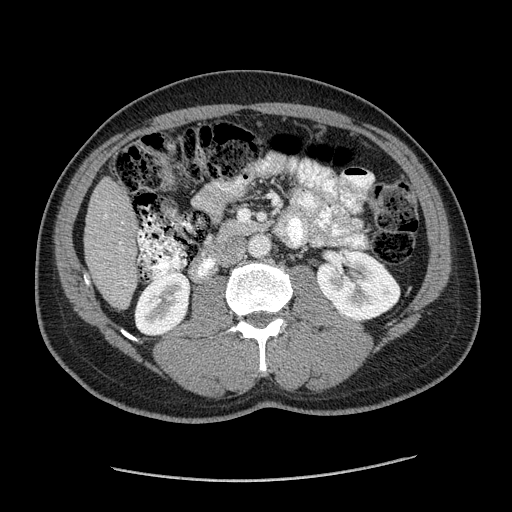
Contrast-enhanced abdominal CT (liver protocol), one axial slice; position 49 of 182 along the scan axis; reconstruction kernel STANDARD; soft-tissue window (W 400 / L 40 HU); 2.5 mm slice thickness; 512 × 512 image matrix, field of view 400 × 400 mm. Case-level facts recorded for this patient, not image findings: diagnosis: hepatocellular carcinoma (patient treated with transarterial chemoembolisation; whether this scan precedes or follows treatment is not stated here); TNM stage (as recorded): Stage-I; Child-Pugh class: A; tumour differentiation: well differentiated.
Structures marked on this image (semi-automatically segmented with operator editing):
- liver parenchyma outside the tumour (the mass and vessels are separate outlines, so this box may not span the whole liver): bounding box <84,178,138,308> (left, top, right, bottom; pixels)
- liver vessels: <105,215,122,244>